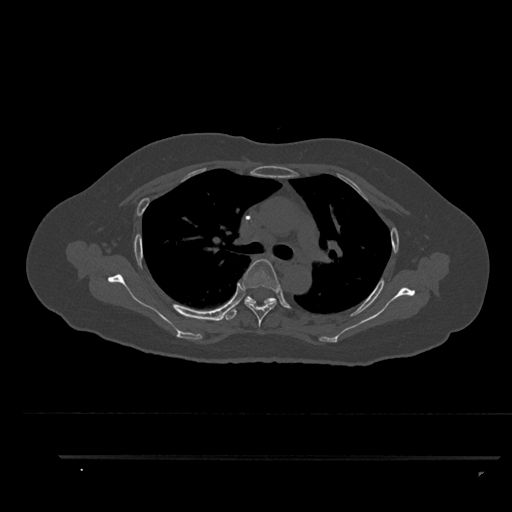
CT including the spine, one axial slice; position 628 of 797 along the scan axis; reconstruction kernel Br40s/3; 120 kVp; bone window (W 1800 / L 400 HU); 0.5 mm slice thickness; 512 × 512 image matrix, field of view 408 × 408 mm. Patient: female, 44 years. From the clinical record (not read from this slice): primary cancer: renal; vertebrae with lytic lesions (as recorded): L1.
Structures marked on this image (semi-automatically segmented with operator editing):
- T4 vertebra: box from (x=242, y=259) to (x=280, y=327) px
- T5 vertebra: (x=225, y=296)–(x=275, y=320)